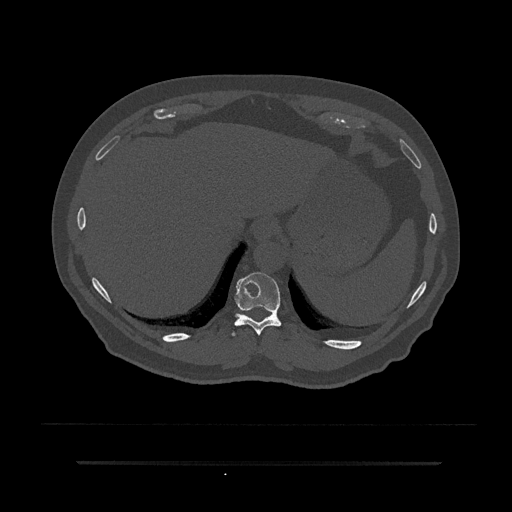
CT including the spine, one axial slice; slice 322 of 797 in the series (ordered by position); 120 kVp; bone window (W 1800 / L 400 HU); 0.5 mm slice thickness; 512 × 512 image matrix, field of view 464 × 464 mm. Male patient, age 59 years. Case-level facts recorded for this patient, not image findings: primary cancer: bile ducts; vertebrae with lytic lesions (as recorded): T10.
Outlined on this slice (semi-automatic segmentation, software-assisted and operator-edited):
- T10 vertebra: bounding box [x1, y1, x2, y2] px = [232, 272, 282, 336]